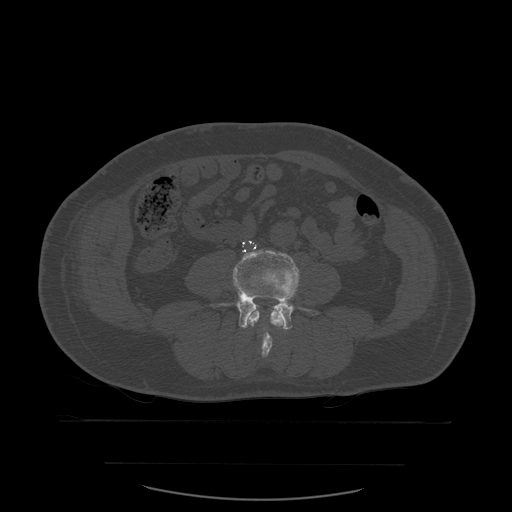
CT including the spine, one axial slice; slice 174 of 590 in the series (ordered by position); bone window (W 1800 / L 400 HU); 1.25 mm slice thickness; 512 × 512 image matrix. Patient age 71 years. From the clinical record (not read from this slice): primary cancer: lung.
Annotated regions visible in this slice (semi-automatic segmentation, software-assisted and operator-edited):
- L3 vertebra: bounding box [x1, y1, x2, y2] px = [247, 311, 285, 358]
- L4 vertebra: [210, 250, 300, 330]